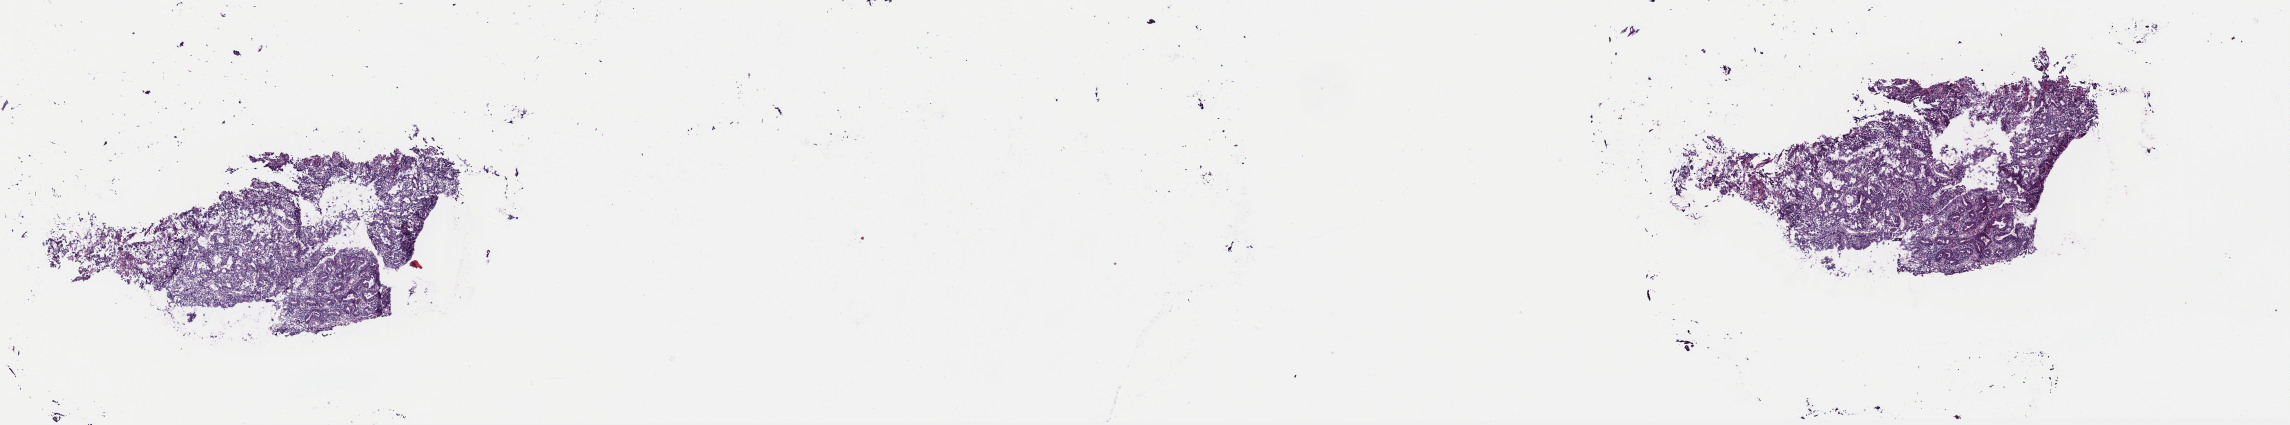
Whole-slide histology image, Hematoxylin and eosin (H&E) stained, whole scanned area (about 18.1 x 3.4 mm, acquisition: 40x scan) shown as a low-resolution overview, frozen section, primary tumour sample from the esophagus. Male patient; age at initial diagnosis 83 years. Histologic grade: GX (grade cannot be assessed). Composition of this section per pathologist review: tumour cells 100%, tumour nuclei 75%, normal cells 0%, stromal cells 0%, necrosis 0%. Inflammatory infiltration, as recorded: lymphocyte infiltration 5%, monocyte infiltration 0%, neutrophil infiltration 0%.
Lymph nodes positive (case pathology): 0 of 12 examined. AJCC pathologic stage: IA (7th edition). TNM: T1 N0 MX. Pathologic diagnosis: Adenocarcinoma, NOS (lower third of esophagus).